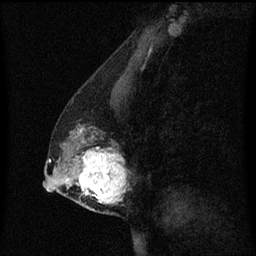
Breast MRI (dynamic contrast-enhanced), one sagittal slice; slice 27 of 60 in the series (ordered by position); dynamic contrast-enhanced series, image 2 of 3 at this slice position (ordered by acquisition); 1.5 T; TE 4.2 ms, TR 8.4 ms; 2 mm slice thickness; 256 × 256 image matrix, field of view 200 × 200 mm. Female patient, age 40 years. From the clinical record (not read from this slice): setting: breast cancer imaged before/during neoadjuvant chemotherapy; receptor status: triple-negative.
Annotated regions visible in this slice (semi-automatic segmentation, software-assisted and operator-edited):
- analysis volume of interest (the breast-tissue region the enhancement analysis was run in; not a lesion): bounding box <60,126,131,215> (left, top, right, bottom; pixels)
- tumour enhancement mask (voxels above the 70 % enhancement threshold inside the analysis volume of interest): <64,128,127,205>